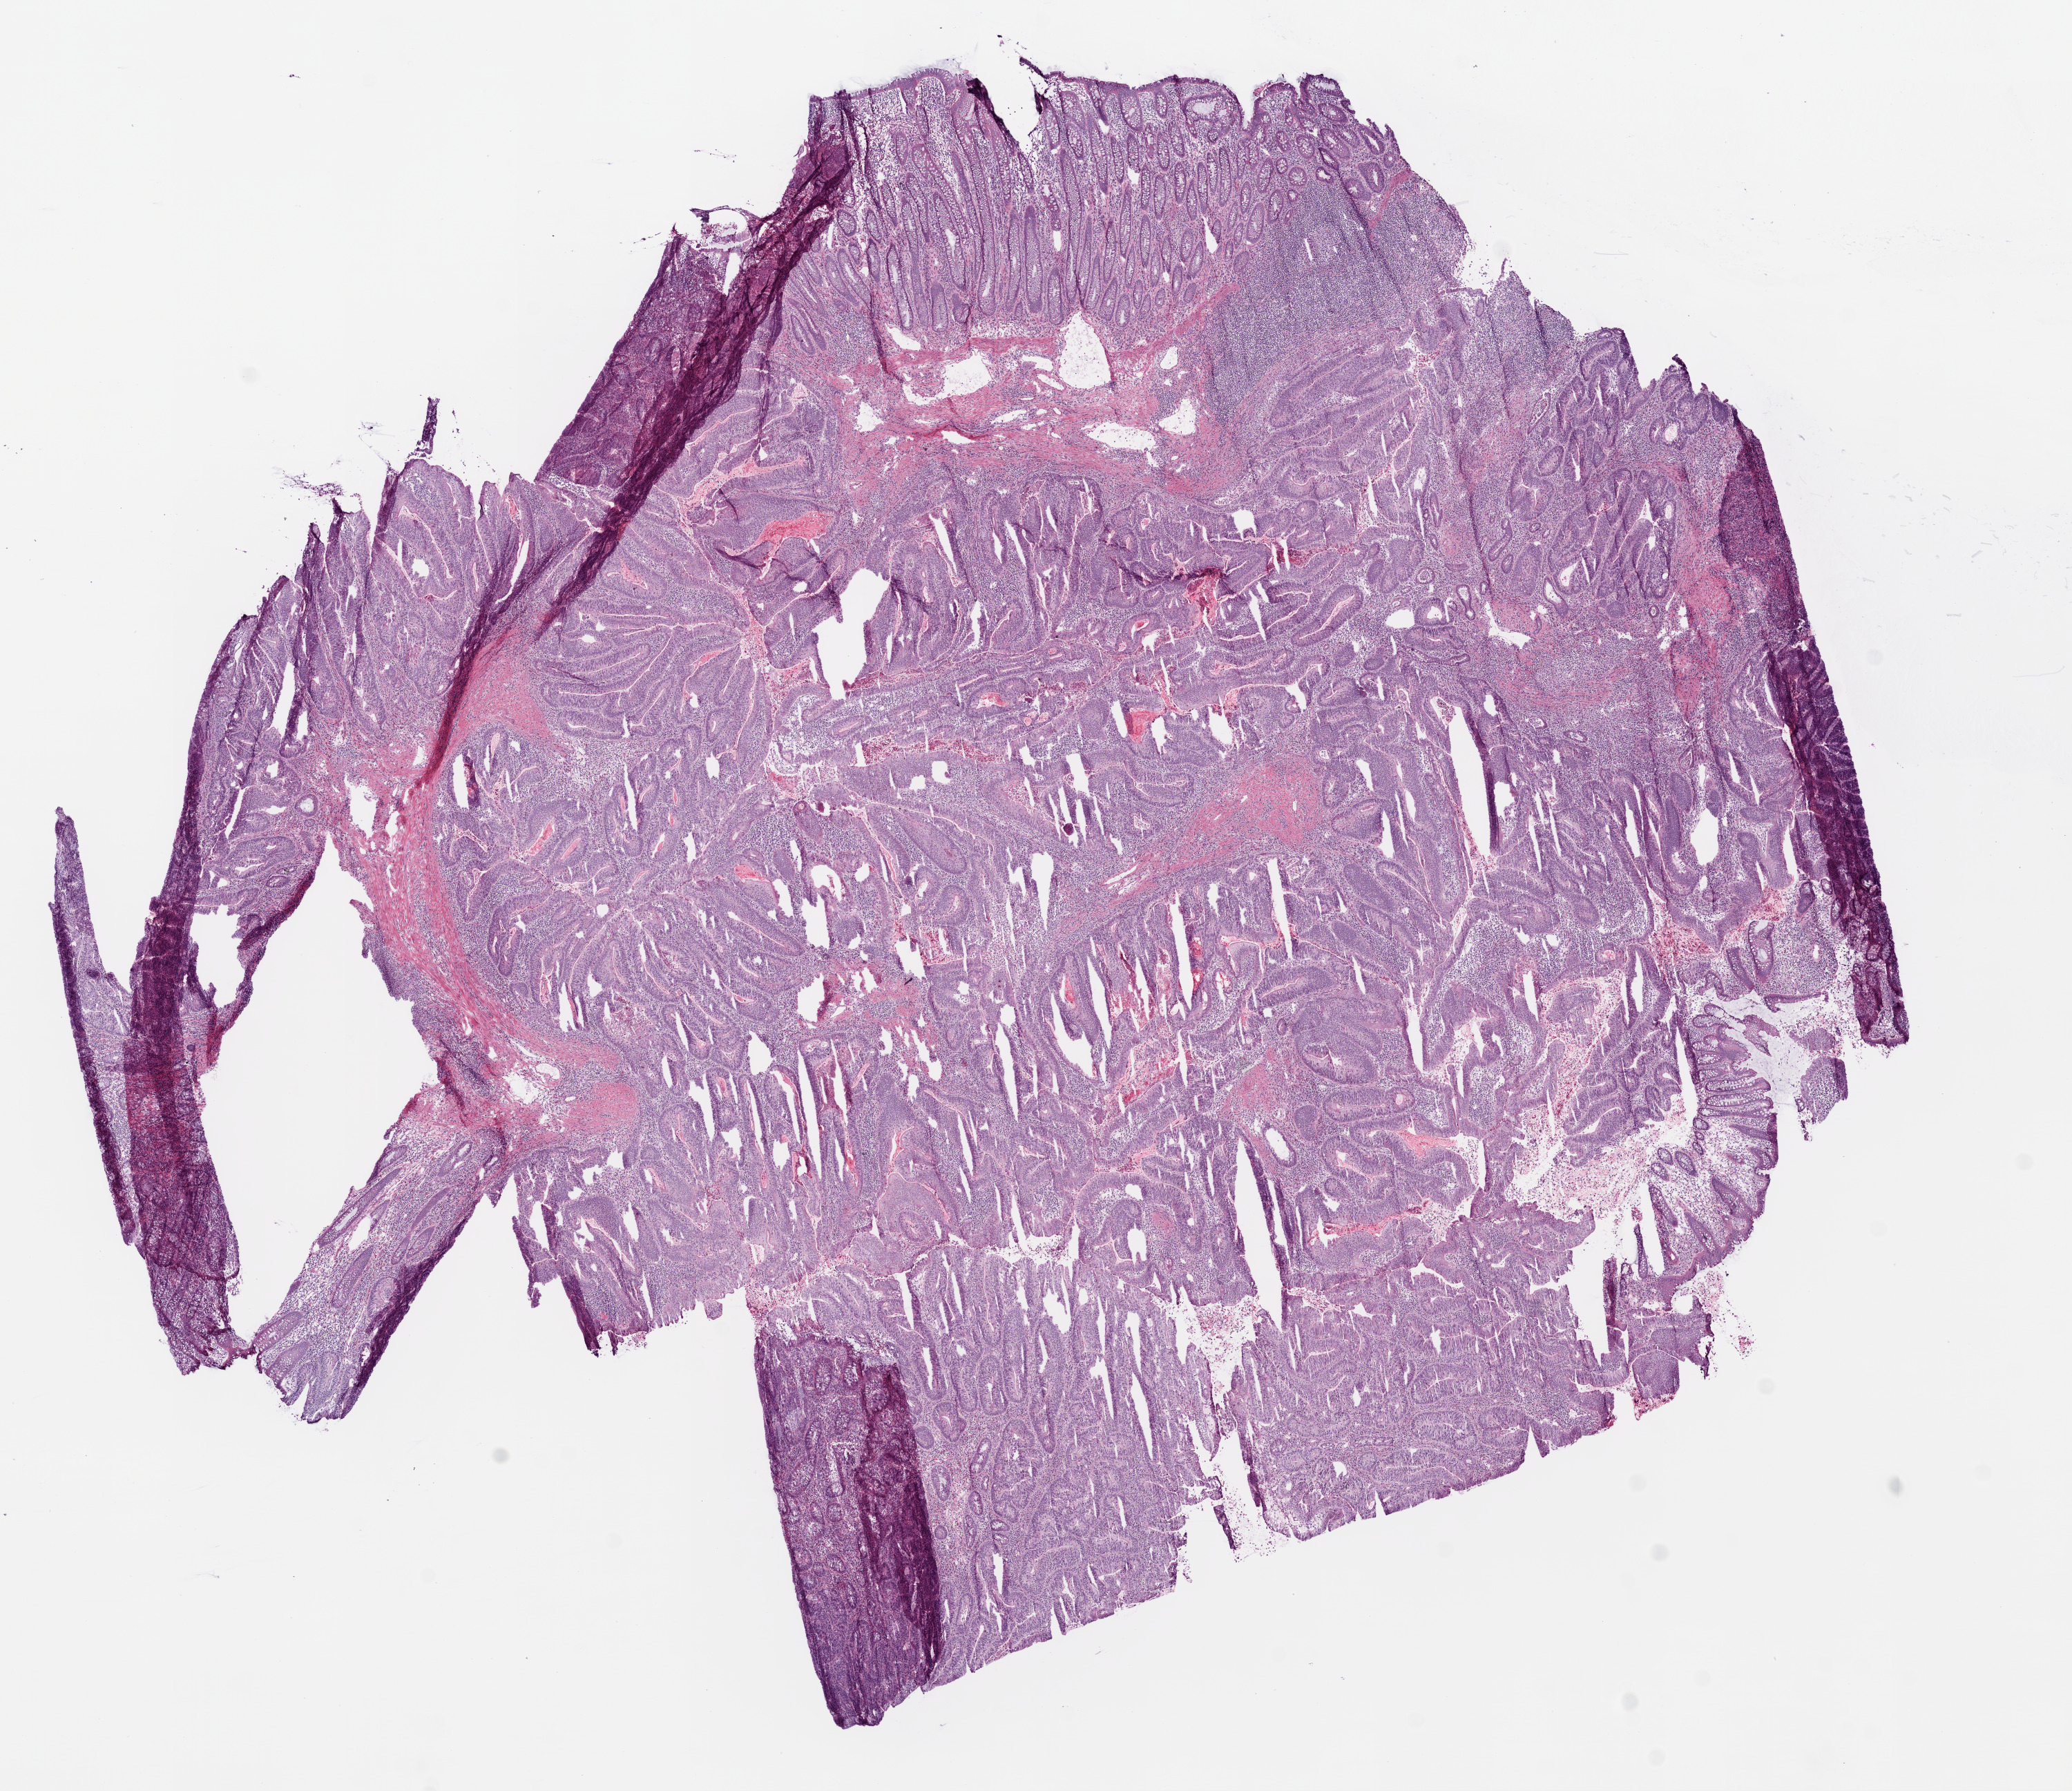
H&E whole-slide image, whole scanned area (about 12.0 x 10.4 mm) shown as a low-resolution overview. Frozen section from the bottom of the tissue portion. Primary tumour sample from the colon. Male patient; age at initial diagnosis 73 years. Composition of this section per pathologist review: tumour cells 80%, tumour nuclei 86%, normal cells 18%, stromal cells 2%, necrosis 0%.
- diagnosis: Adenocarcinoma, NOS
- AJCC pathologic stage: I (5th edition)
- lymph nodes positive (case pathology): 0 of 27 examined